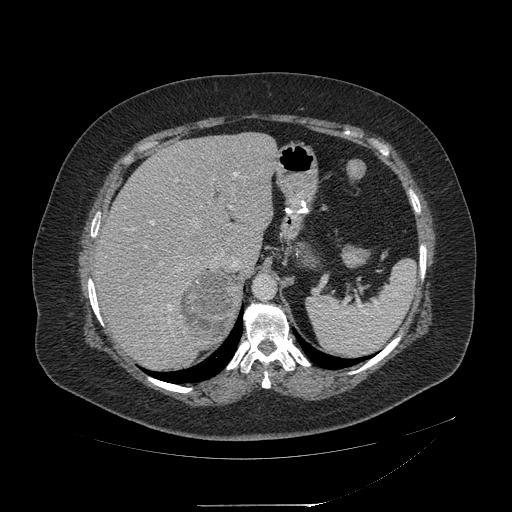
Contrast-enhanced abdominal CT, one axial slice. Position 156 of 217 along the scan axis. Intravenous contrast given. Soft-tissue window (W 400 / L 40 HU). 512 × 512 image matrix, field of view 453 × 453 mm. Female patient, age 55 years. Case-level facts recorded for this patient, not image findings: diagnosis: adrenocortical carcinoma; tumour side: right adrenal; tumour size at pathology: 11 cm; Ki-67 index: 20 %; stage (as recorded): 2.
Structures marked on this image (semi-automatically segmented with operator editing):
- mass: bounding box [x1, y1, x2, y2] px = [181, 270, 237, 340]